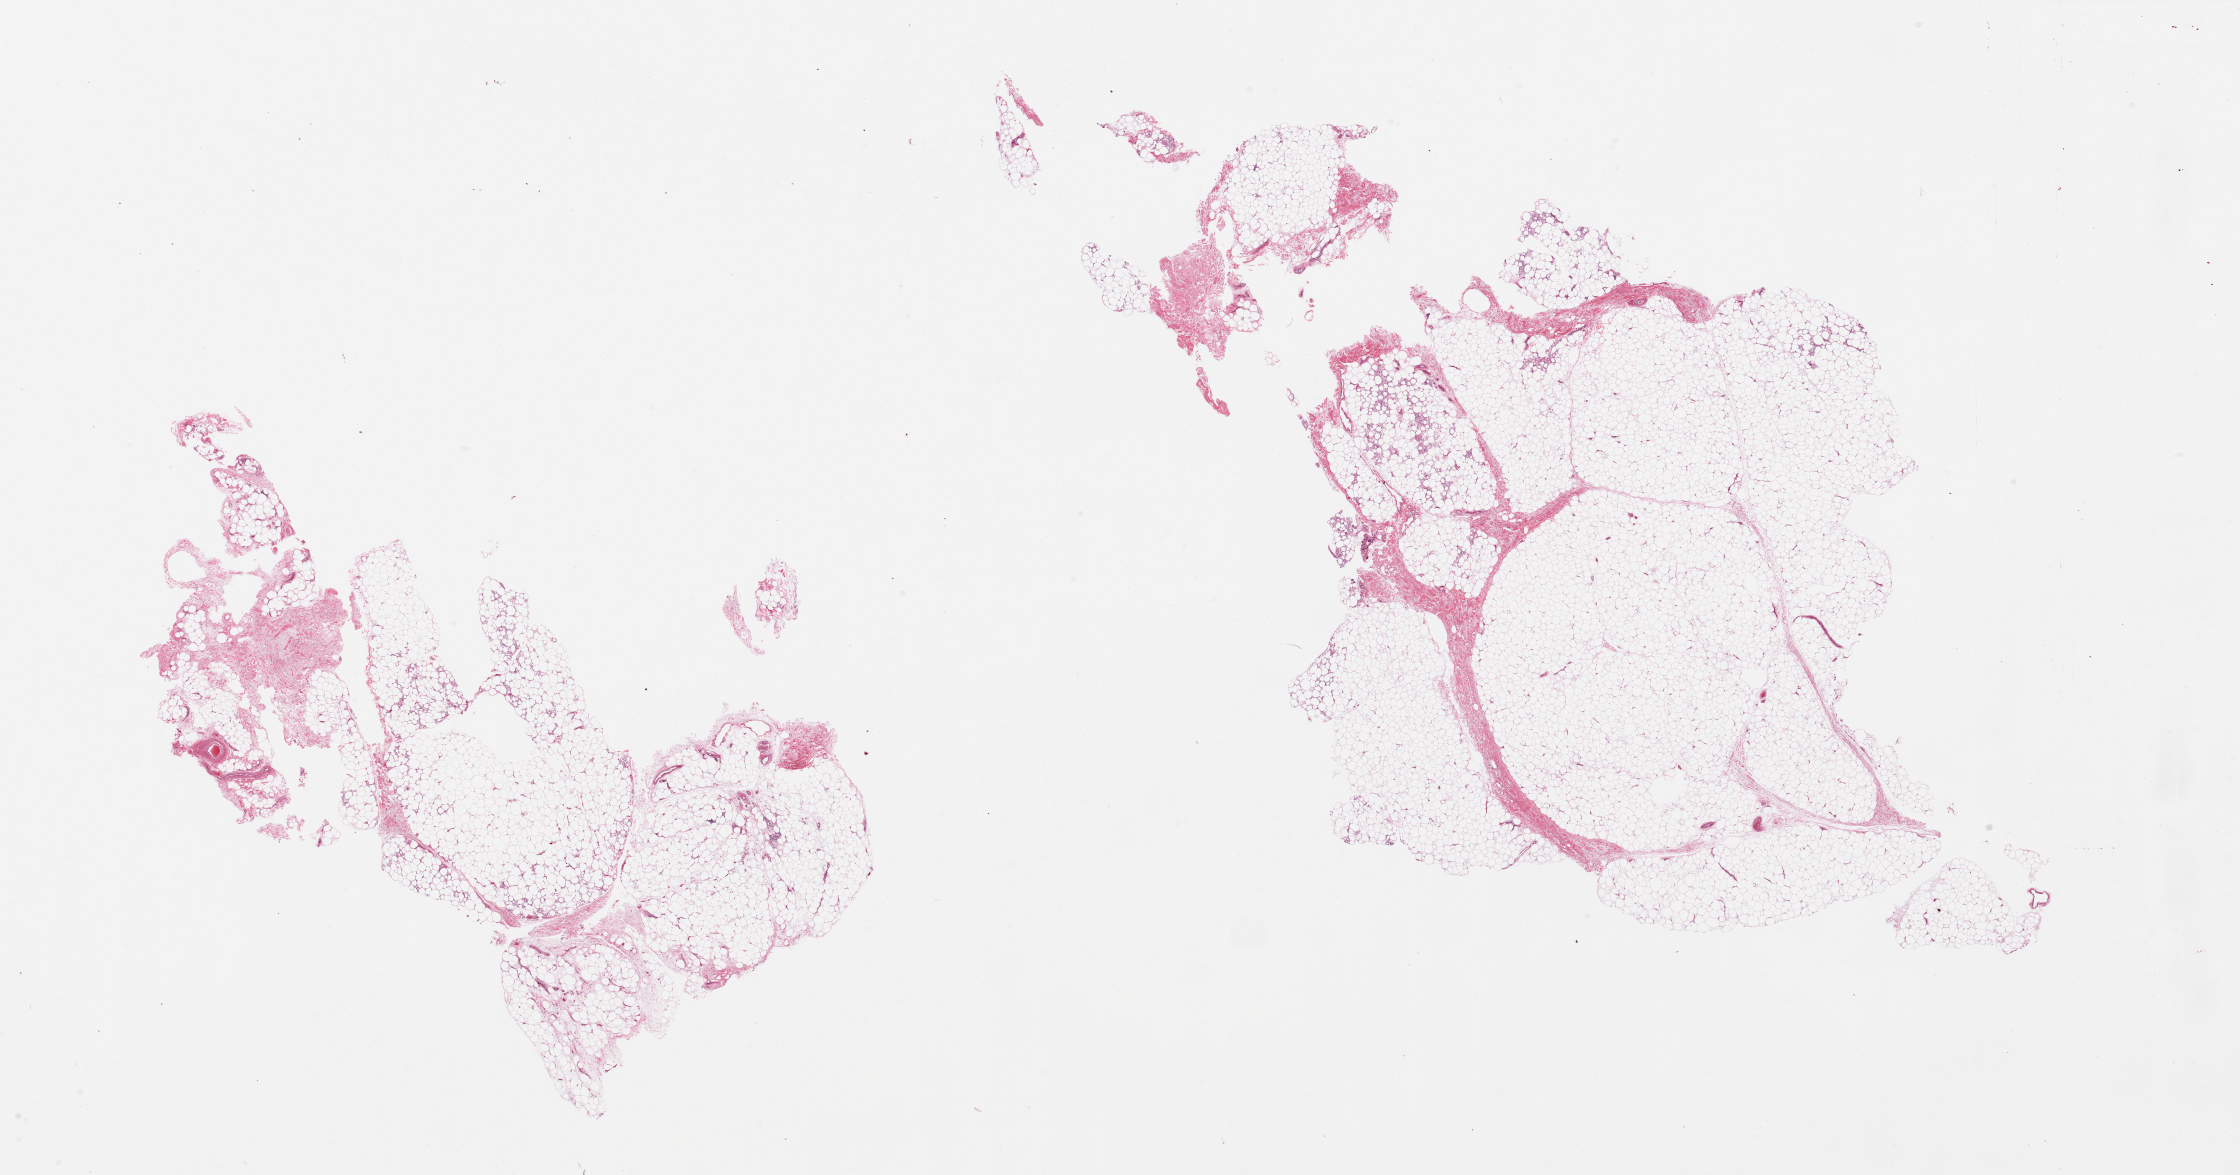
Digitized haematoxylin and eosin-stained section, brightfield, shown as a low-resolution overview of the whole scanned area (about 35.4 x 18.6 mm, slide scanned at 20x). PAXgene-fixed paraffin-embedded (PFPE) section. Target tissue: adipose tissue. Donor tissue sample. Donor sex: male.
Review note (as recorded): 2 pieces.